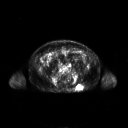
FDG PET of an extremity soft-tissue mass (from a PET/CT study), one axial slice. Slice 95 of 267 in the series (ordered by position). 128 × 128 image matrix, field of view 700 × 700 mm. Patient: male, 61 years. Case-level facts recorded for this patient, not image findings: histological type: pleiomorphic leiomyosarcoma; grade: high; site of the primary tumour: left buttock.
Outlined on this slice (expert contour drawn on MRI and transferred to this co-registered scan by the dataset authors):
- gross tumour volume including surrounding oedema: bounding box [x1, y1, x2, y2] px = [76, 85, 83, 91]
- gross tumour volume (mass): [76, 85, 82, 91]